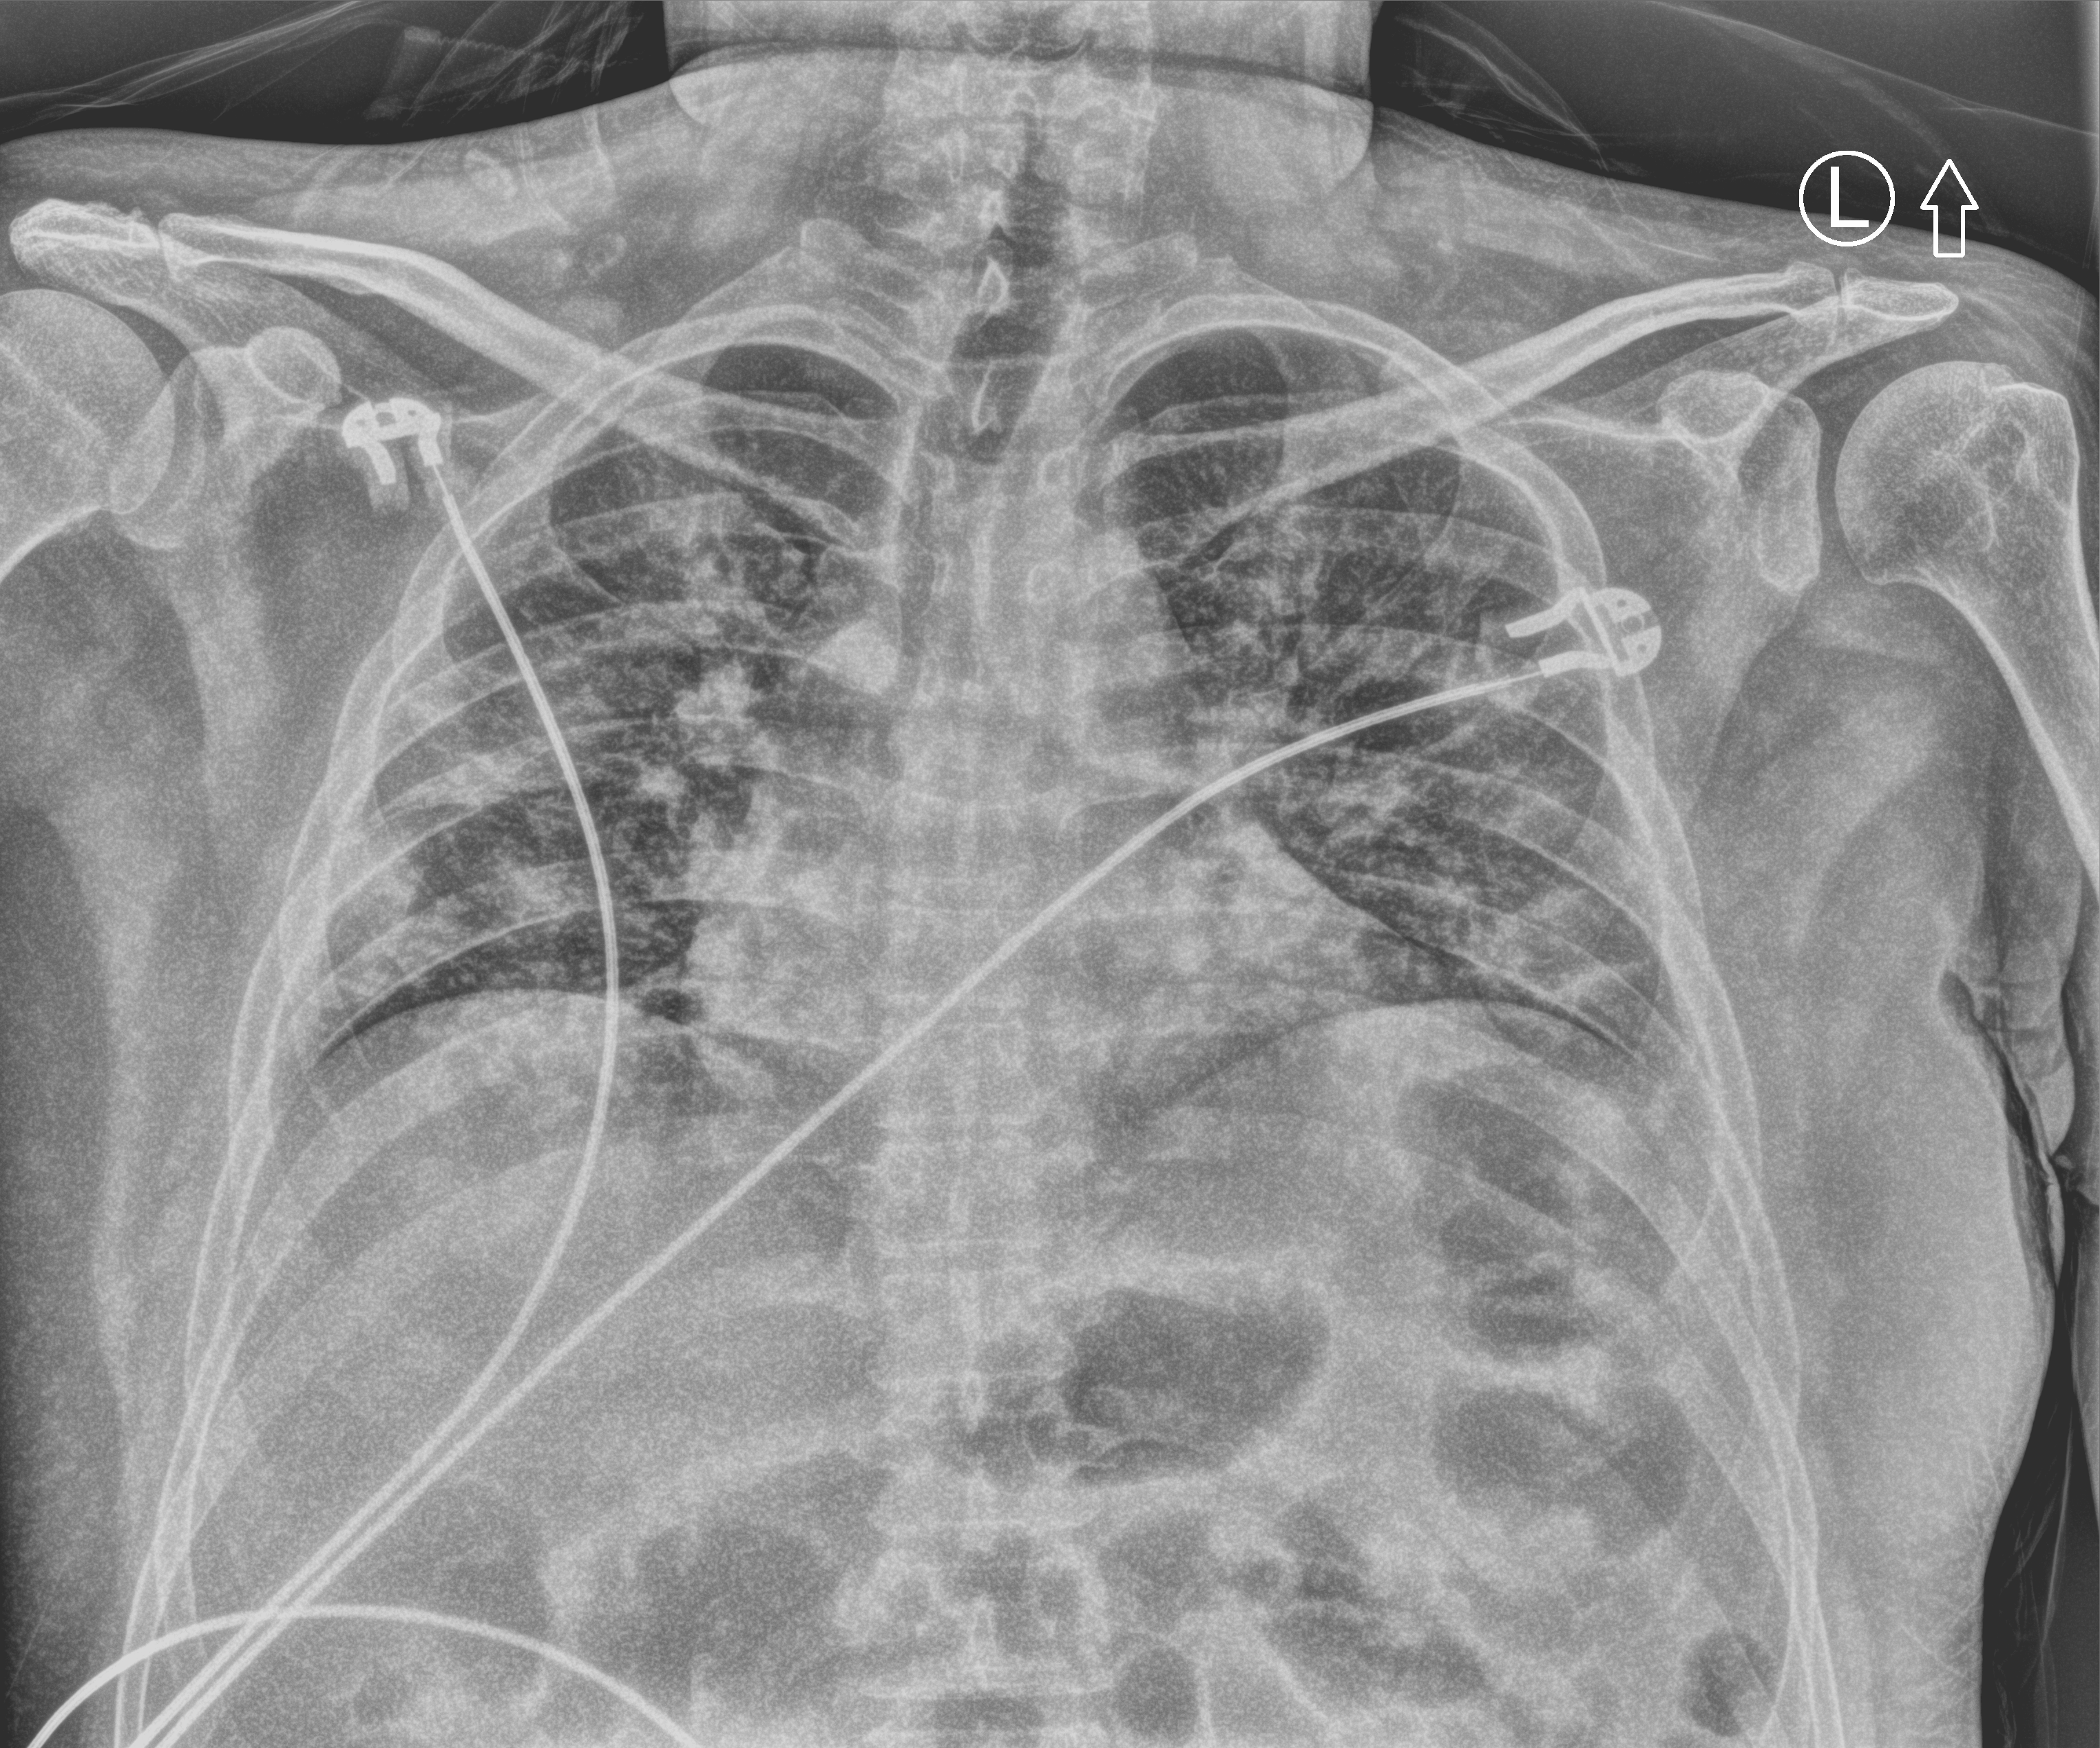
Bedside chest radiograph (computed radiography). Male patient hospitalised with COVID-19, age 18–59 years.
Admission-level facts for this patient (not findings on this image; timing relative to this image not recorded):
- smoking status (admission record): never
- length of hospital stay: 10 days
- admitted to intensive care during this hospital stay: no